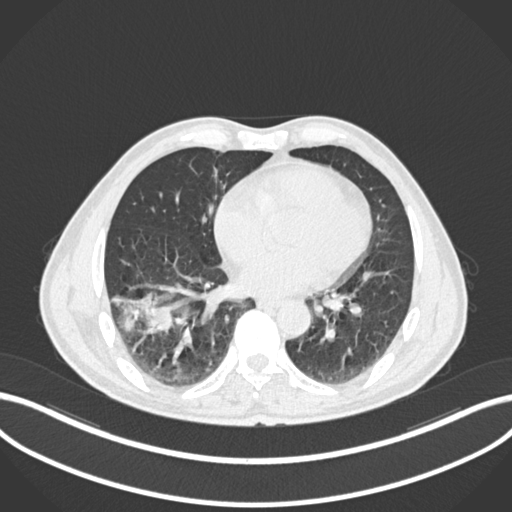
Chest CT, one axial slice. Slice 69 of 208 in the series (ordered by position). Reconstruction kernel B30f. 120 kVp. Lung window (W 1500 / L -600 HU). 1 mm slice thickness. 512 × 512 image matrix, field of view 400 × 400 mm. Patient: male, 58 years. Case-level facts recorded for this patient, not image findings: clinical TNM (as recorded): T3 N0 M0; histopathological grade: G2.
Structures marked on this image (bounding box drawn by a radiologist):
- lung tumour (recorded histology: squamous cell carcinoma): bounding box (x1, y1, x2, y2) in pixels: (112, 286, 180, 339)